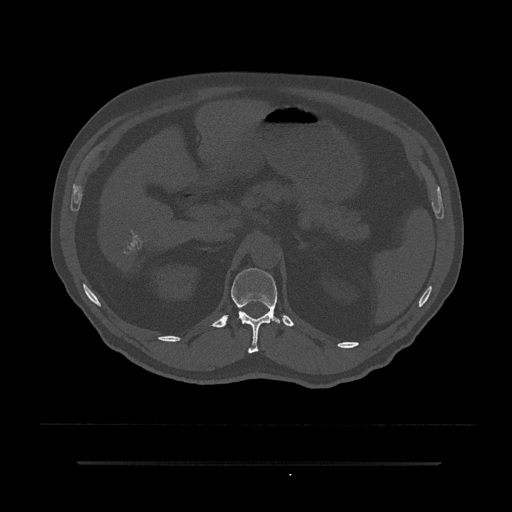
CT including the spine, one axial slice; slice 205 of 797 in the series (ordered by position); reconstruction kernel Br40s/3; 120 kVp; bone window (W 1800 / L 400 HU); 512 × 512 image matrix, field of view 464 × 464 mm. Patient: male, 59 years. From the clinical record (not read from this slice): primary cancer: bile ducts; vertebrae with lytic lesions (as recorded): T10.
Annotated regions visible in this slice (semi-automatic segmentation, software-assisted and operator-edited):
- T12 vertebra: bounding box <231,268,281,353> (left, top, right, bottom; pixels)